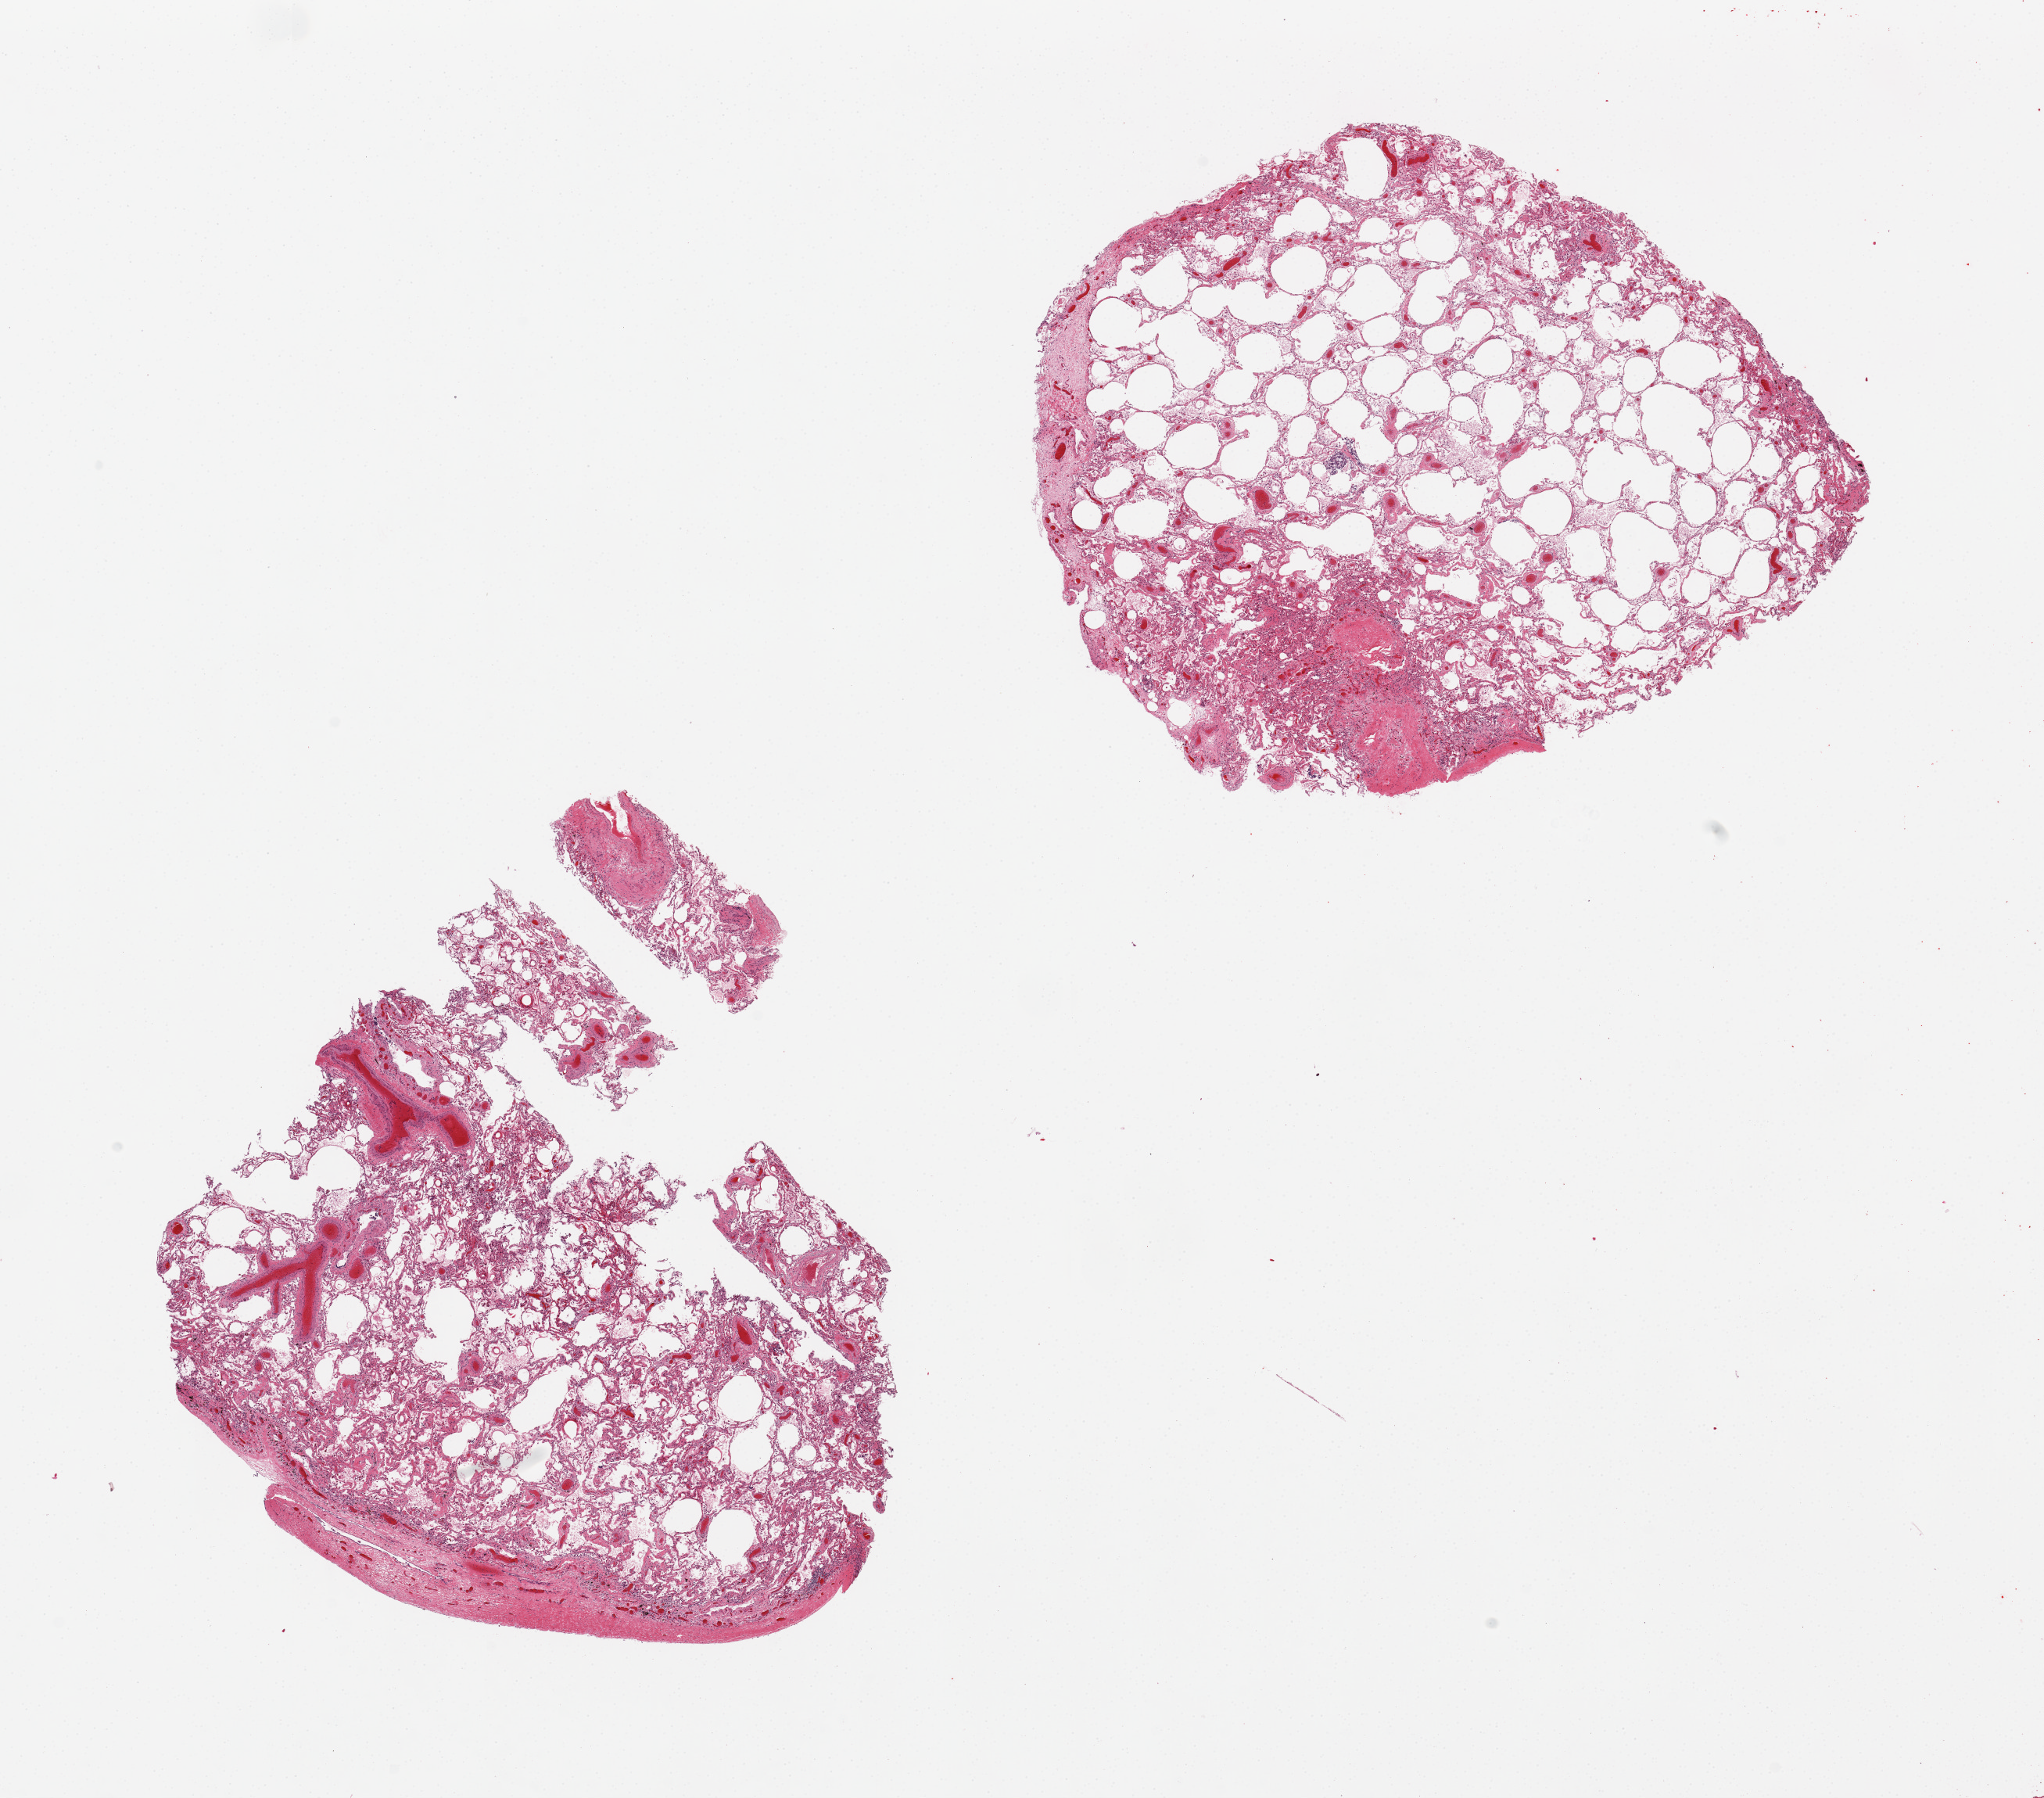
Digitized hematoxylin and eosin (H&E)-stained section — whole scanned area (about 20.7 x 18.2 mm, slide scanned at 20x) shown as a low-resolution overview. PAXgene-fixed, paraffin-embedded tissue. Sampled site (target tissue): lung. Tissue donor sample.
Reviewer comment on this tissue sample: 2 pieces moderate edema, emphysematous changes.